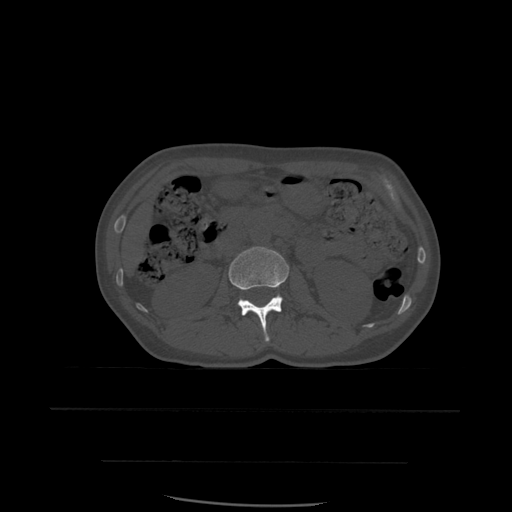
CT including the spine, one axial slice. Bone window (W 1800 / L 400 HU). 512 × 512 image matrix, field of view 392 × 392 mm. Patient age 48 years. Case-level facts recorded for this patient, not image findings: primary cancer: lung; vertebrae with lytic lesions (as recorded): T11.
Annotated regions visible in this slice (semi-automatically segmented with operator editing):
- L2 vertebra: box from (x=229, y=247) to (x=289, y=342) px